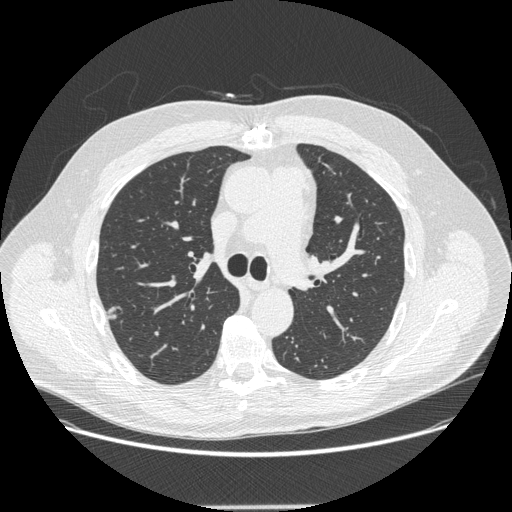
Axial slice from a low-dose chest CT screening exam, third screening round (two years after baseline), lung window (W 1500 / L -600 HU), 1.25 mm slice thickness, standard (soft-tissue) reconstruction kernel (STANDARD), 120 kVp, slice 81 of 265 in the series. Male, age 62 years at enrolment. Current smoker at enrolment.
- Expert-annotated lung lesion, bounding box (x1, y1, x2, y2) in pixels: (94, 299, 132, 330).
- Screening reader's record for this exam (one nodule recorded; not confirmed to be the boxed lesion): non-calcified nodule or mass ≥4 mm, right upper lobe, 12 × 11 mm, smooth margins, soft tissue attenuation, pre-existing on the prior screen: yes; interval growth: yes.
- Later outcome: lung cancer diagnosed 112 days after this screen — adenocarcinoma, NOS, right upper lobe, moderately differentiated (G2), stage IA (AJCC 6th edition), 12 mm at pathology.